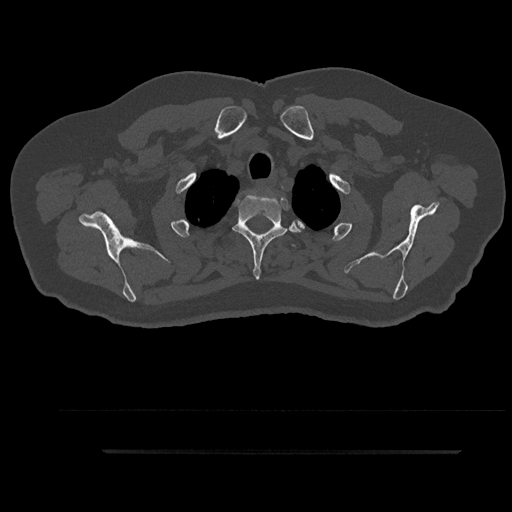
CT including the spine, one axial slice. Slice 755 of 797 in the series (ordered by position). Reconstruction kernel Br40s/3. 120 kVp. Bone window (W 1800 / L 400 HU). 0.5 mm slice thickness. 512 × 512 image matrix, field of view 432 × 432 mm. Male patient, age 63 years. Case-level facts recorded for this patient, not image findings: primary cancer: renal; vertebrae with lytic lesions (as recorded): T8.
Structures marked on this image (semi-automatic segmentation, software-assisted and operator-edited):
- T2 vertebra: bounding box (x1, y1, x2, y2) in pixels: (232, 194, 305, 279)
- T3 vertebra: (218, 223, 296, 250)